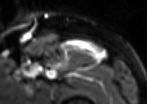
MRI of an extremity soft-tissue mass, one axial slice; position 79 of 85 along the scan axis; T2-weighted fat-saturated; MR volume resampled by the dataset authors to the PET/CT grid (not the native acquisition matrix); 3.27 mm slice thickness; 147 × 104 image matrix. Male patient. From the clinical record (not read from this slice): histological type: extraskeletal osteosarcoma; grade: high; site of the primary tumour: thigh.
Outlined on this slice (expert contour drawn on MRI and transferred to this co-registered scan by the dataset authors):
- gross tumour volume (mass): bounding box (x1, y1, x2, y2) in pixels: (67, 40, 107, 61)